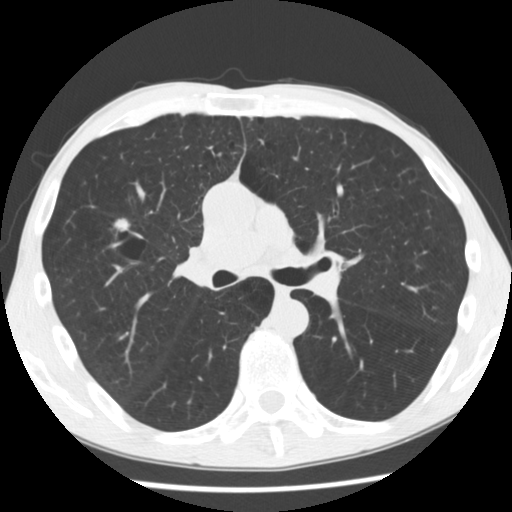
Axial slice from a low-dose chest CT screening exam; baseline annual screen; lung window (W 1500 / L -600 HU); standard (soft-tissue) reconstruction kernel (STANDARD); 120 kVp; slice 125 of 292 in the series; 512 × 512 image matrix. Male, age 56 years at enrolment. Current smoker at enrolment.
Lesion marked by an expert reader, box from (x=99, y=206) to (x=151, y=251) px. The screening reader recorded 2 non-calcified nodules or masses ≥4 mm on this exam; which of them this box marks is not recorded. Official screen result: positive, change unspecified: nodule(s) >= 4 mm or enlarging nodule(s), mass(es), or other non-specific abnormalities suspicious for lung cancer. Later outcome: lung cancer diagnosed 476 days after this screen (after the second annual screen) — squamous cell carcinoma, NOS, right upper lobe, right middle lobe, well differentiated (G1), stage IA (AJCC 6th edition), 27 mm at pathology.